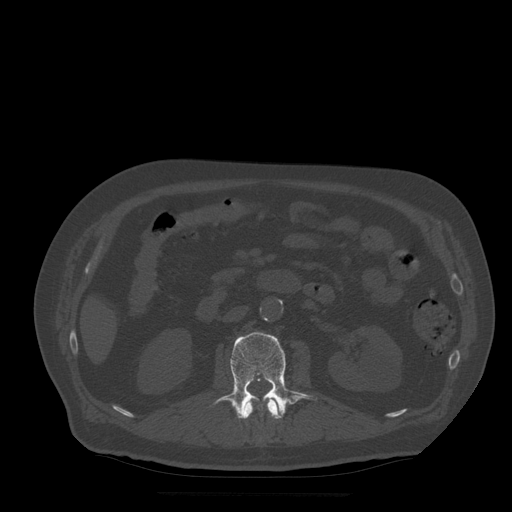
CT including the spine, one axial slice. Bone window (W 1800 / L 400 HU). 1.25 mm slice thickness. 512 × 512 image matrix, field of view 420 × 420 mm. Patient age 72 years. From the clinical record (not read from this slice): primary cancer: prostate.
Annotated regions visible in this slice (semi-automatic segmentation, software-assisted and operator-edited):
- L1 vertebra: bounding box <242,398,281,441> (left, top, right, bottom; pixels)
- L2 vertebra: <214,332,317,419>